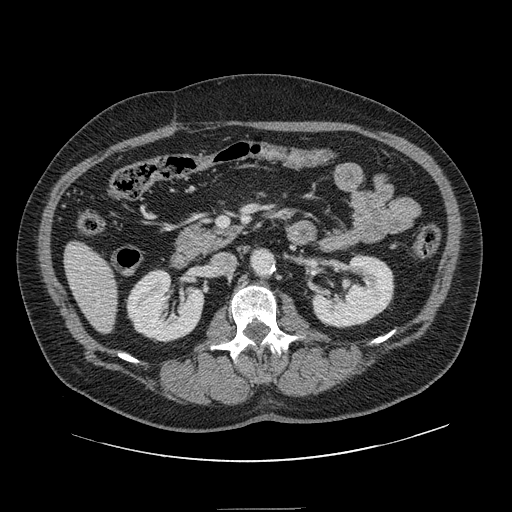
Contrast-enhanced abdominal CT, one axial slice. Slice 46 of 154 in the series (ordered by position). Soft-tissue window (W 400 / L 40 HU). 512 × 512 image matrix, field of view 451 × 451 mm. Male patient, age 61 years. Case-level facts recorded for this patient, not image findings: diagnosis: colorectal cancer liver metastases, imaged before liver resection.
Outlined on this slice (outlined manually by an expert reader):
- hepatic veins: bounding box (x1, y1, x2, y2) in pixels: (82, 268, 99, 295)
- liver: (66, 243, 118, 332)
- planned liver remnant (the part of the liver to remain after resection): (66, 243, 118, 332)